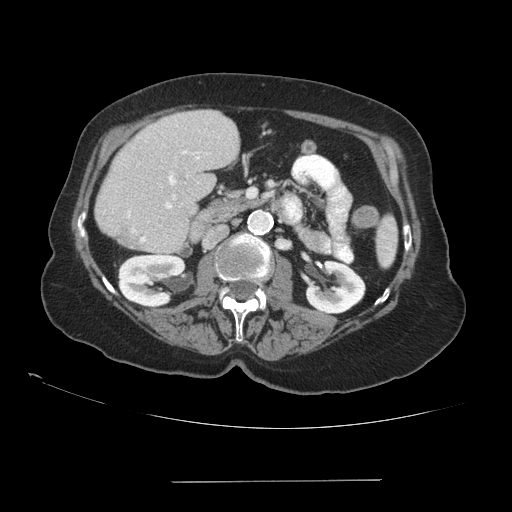
Contrast-enhanced abdominal CT (liver protocol), one axial slice. Slice 37 of 89 in the series (ordered by position). 140 kVp. Soft-tissue window (W 400 / L 40 HU). 512 × 512 image matrix, field of view 400 × 400 mm. From the clinical record (not read from this slice): diagnosis: hepatocellular carcinoma (patient treated with transarterial chemoembolisation; whether this scan precedes or follows treatment is not stated here); TNM stage (as recorded): Stage-IVA; Child-Pugh class: A; tumour differentiation: poorly differentiated.
Structures marked on this image (semi-automatically segmented with operator editing):
- liver parenchyma outside the tumour (the mass and vessels are separate outlines, so this box may not span the whole liver): bounding box <95,110,238,254> (left, top, right, bottom; pixels)
- liver vessels: <129,151,199,242>